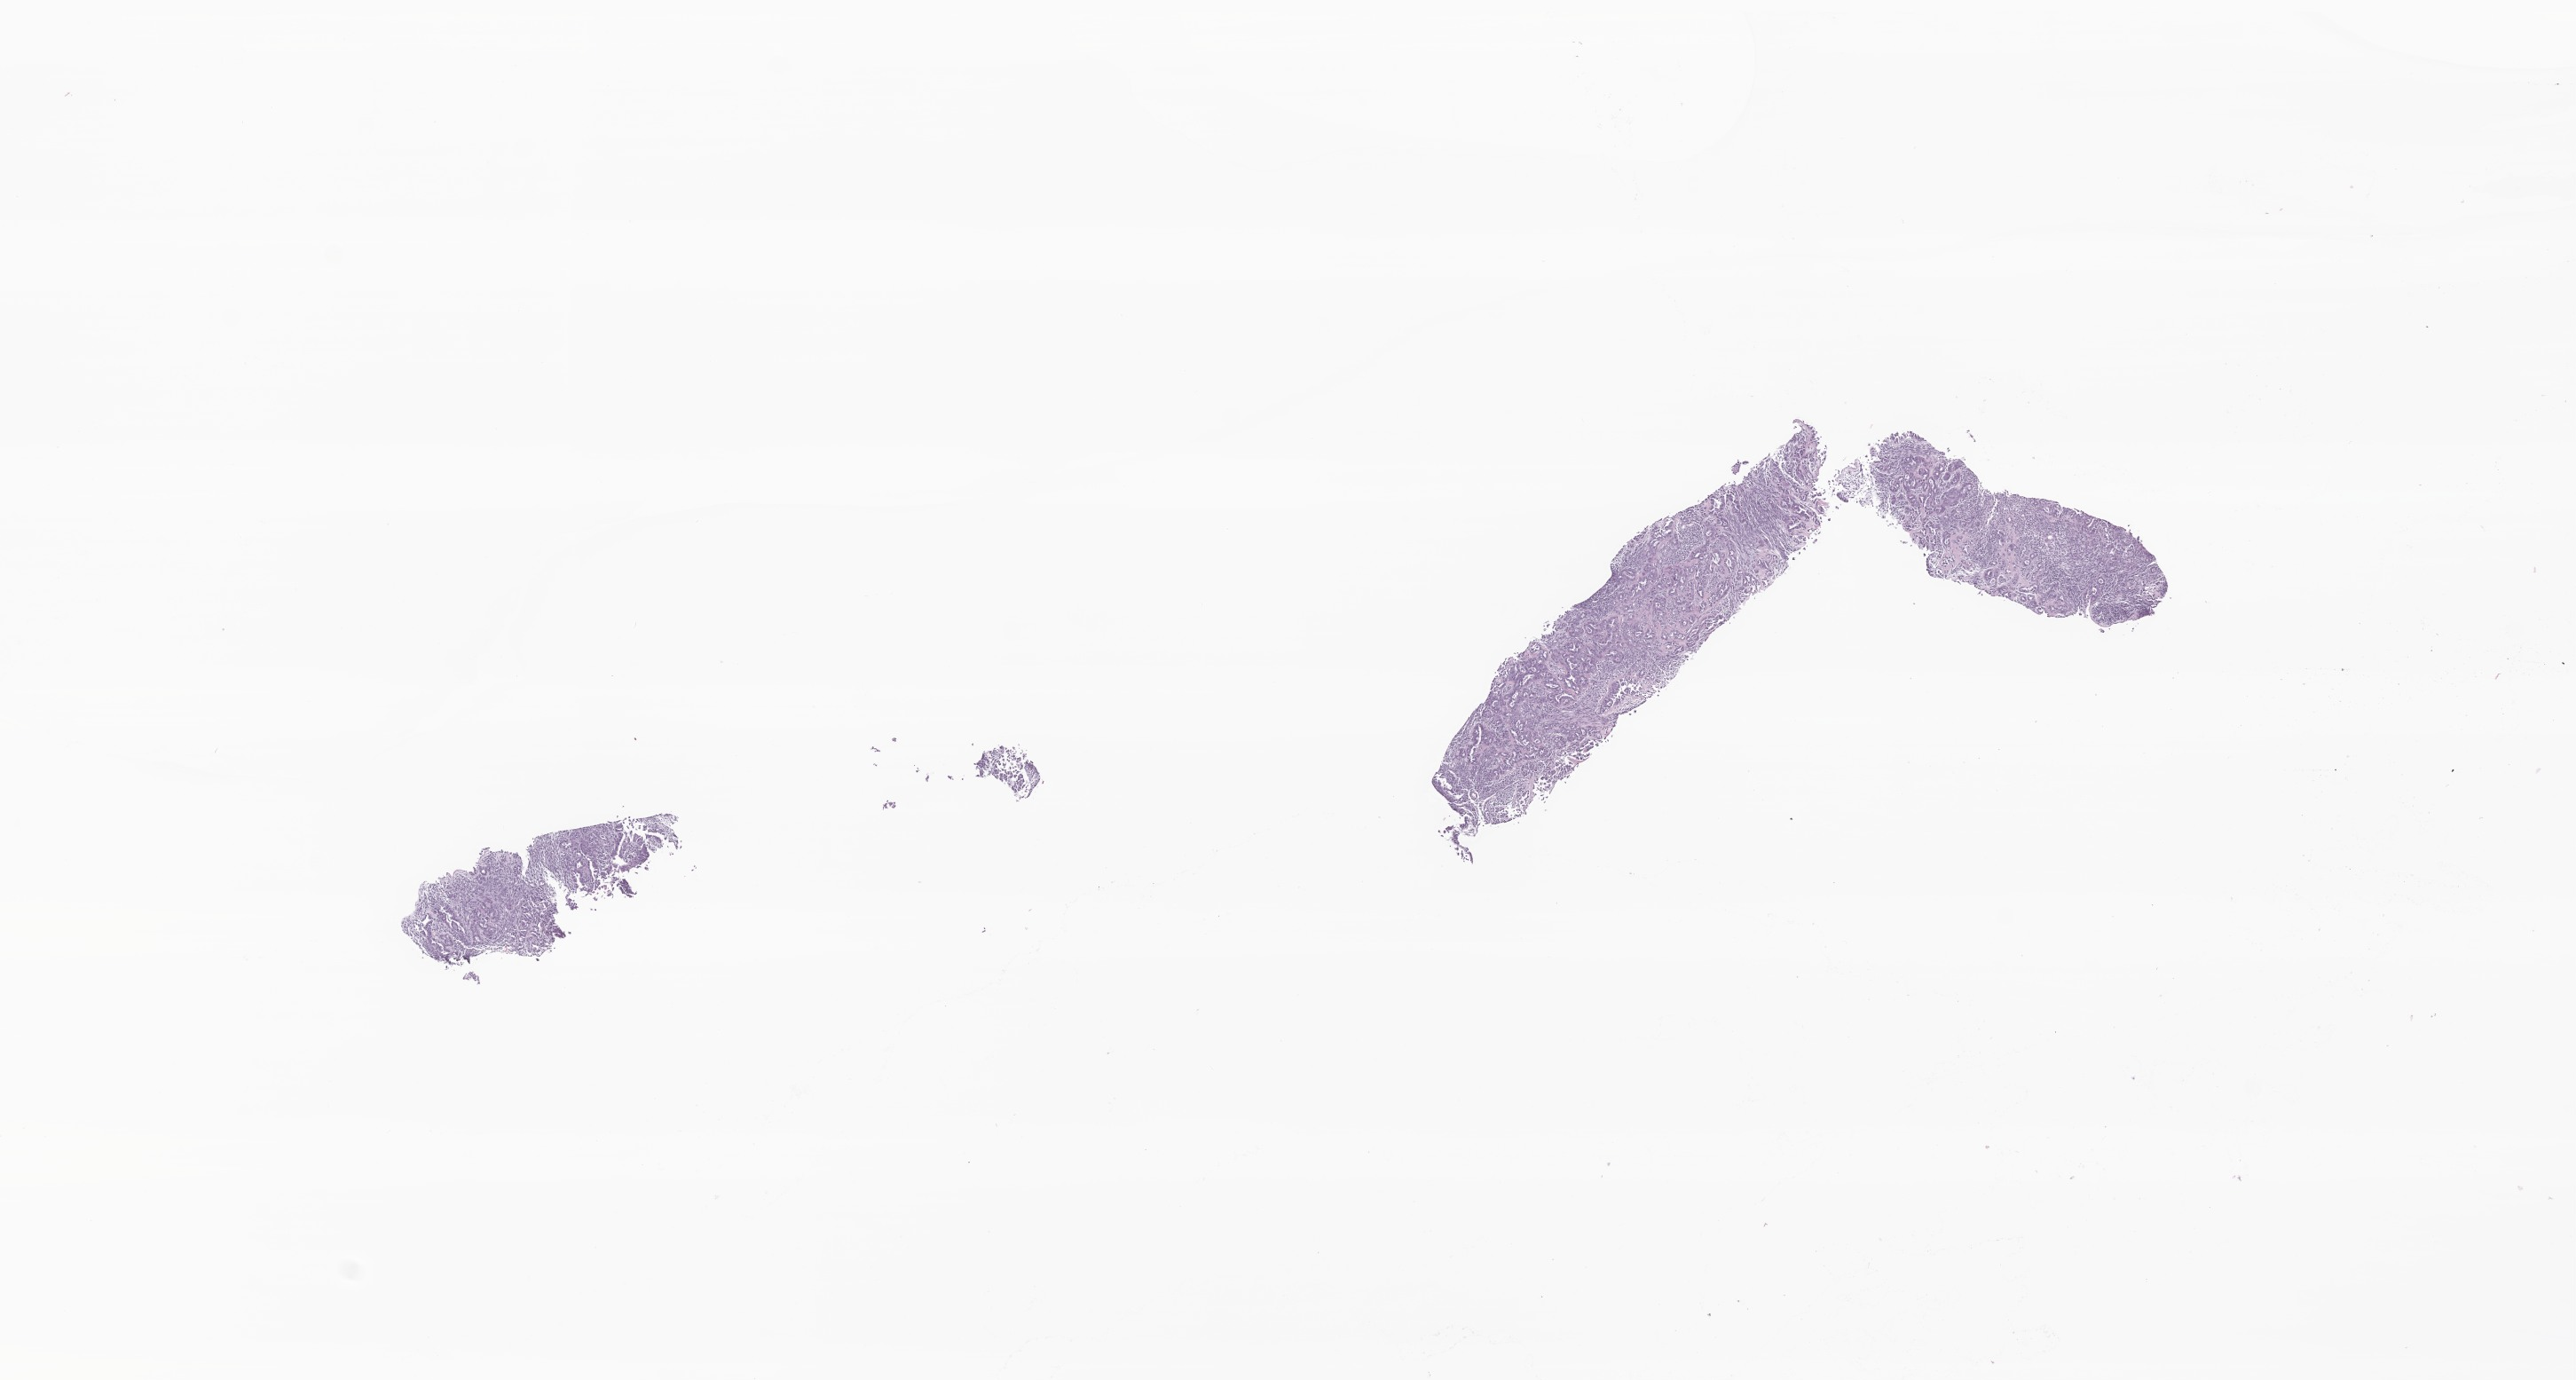
Haematoxylin and eosin whole-slide image of tumor tissue from the upper limb, a low-resolution overview of the entire scanned area, about 12.2 x 6.6 mm; FFPE section. Patient male; age 171 months (14 years 3 months).
Diagnosis: Synovial sarcoma, NOS.